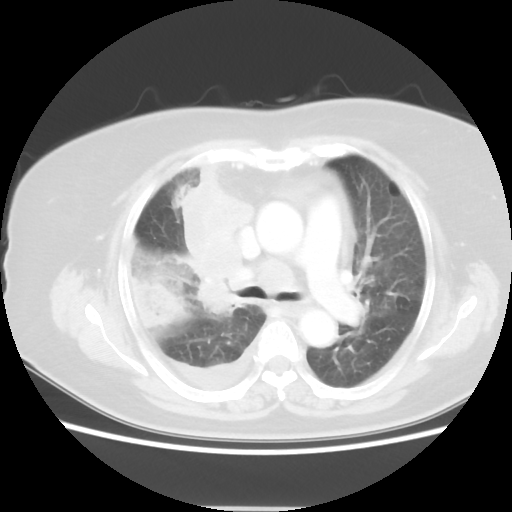
Chest CT, one axial slice. Slice 31 of 48 in the series (ordered by position). Reconstruction kernel STANDARD. Lung window (W 1500 / L -600 HU). 5 mm slice thickness. 512 × 512 image matrix, field of view 360 × 360 mm. Female patient, age 73 years. Case-level facts recorded for this patient, not image findings: clinical TNM (as recorded): T3 N3 M1b; histopathological grade: G3.
Outlined on this slice (bounding box drawn by a radiologist):
- lung tumour (recorded histology: small cell carcinoma): bounding box <174,170,259,284> (left, top, right, bottom; pixels)